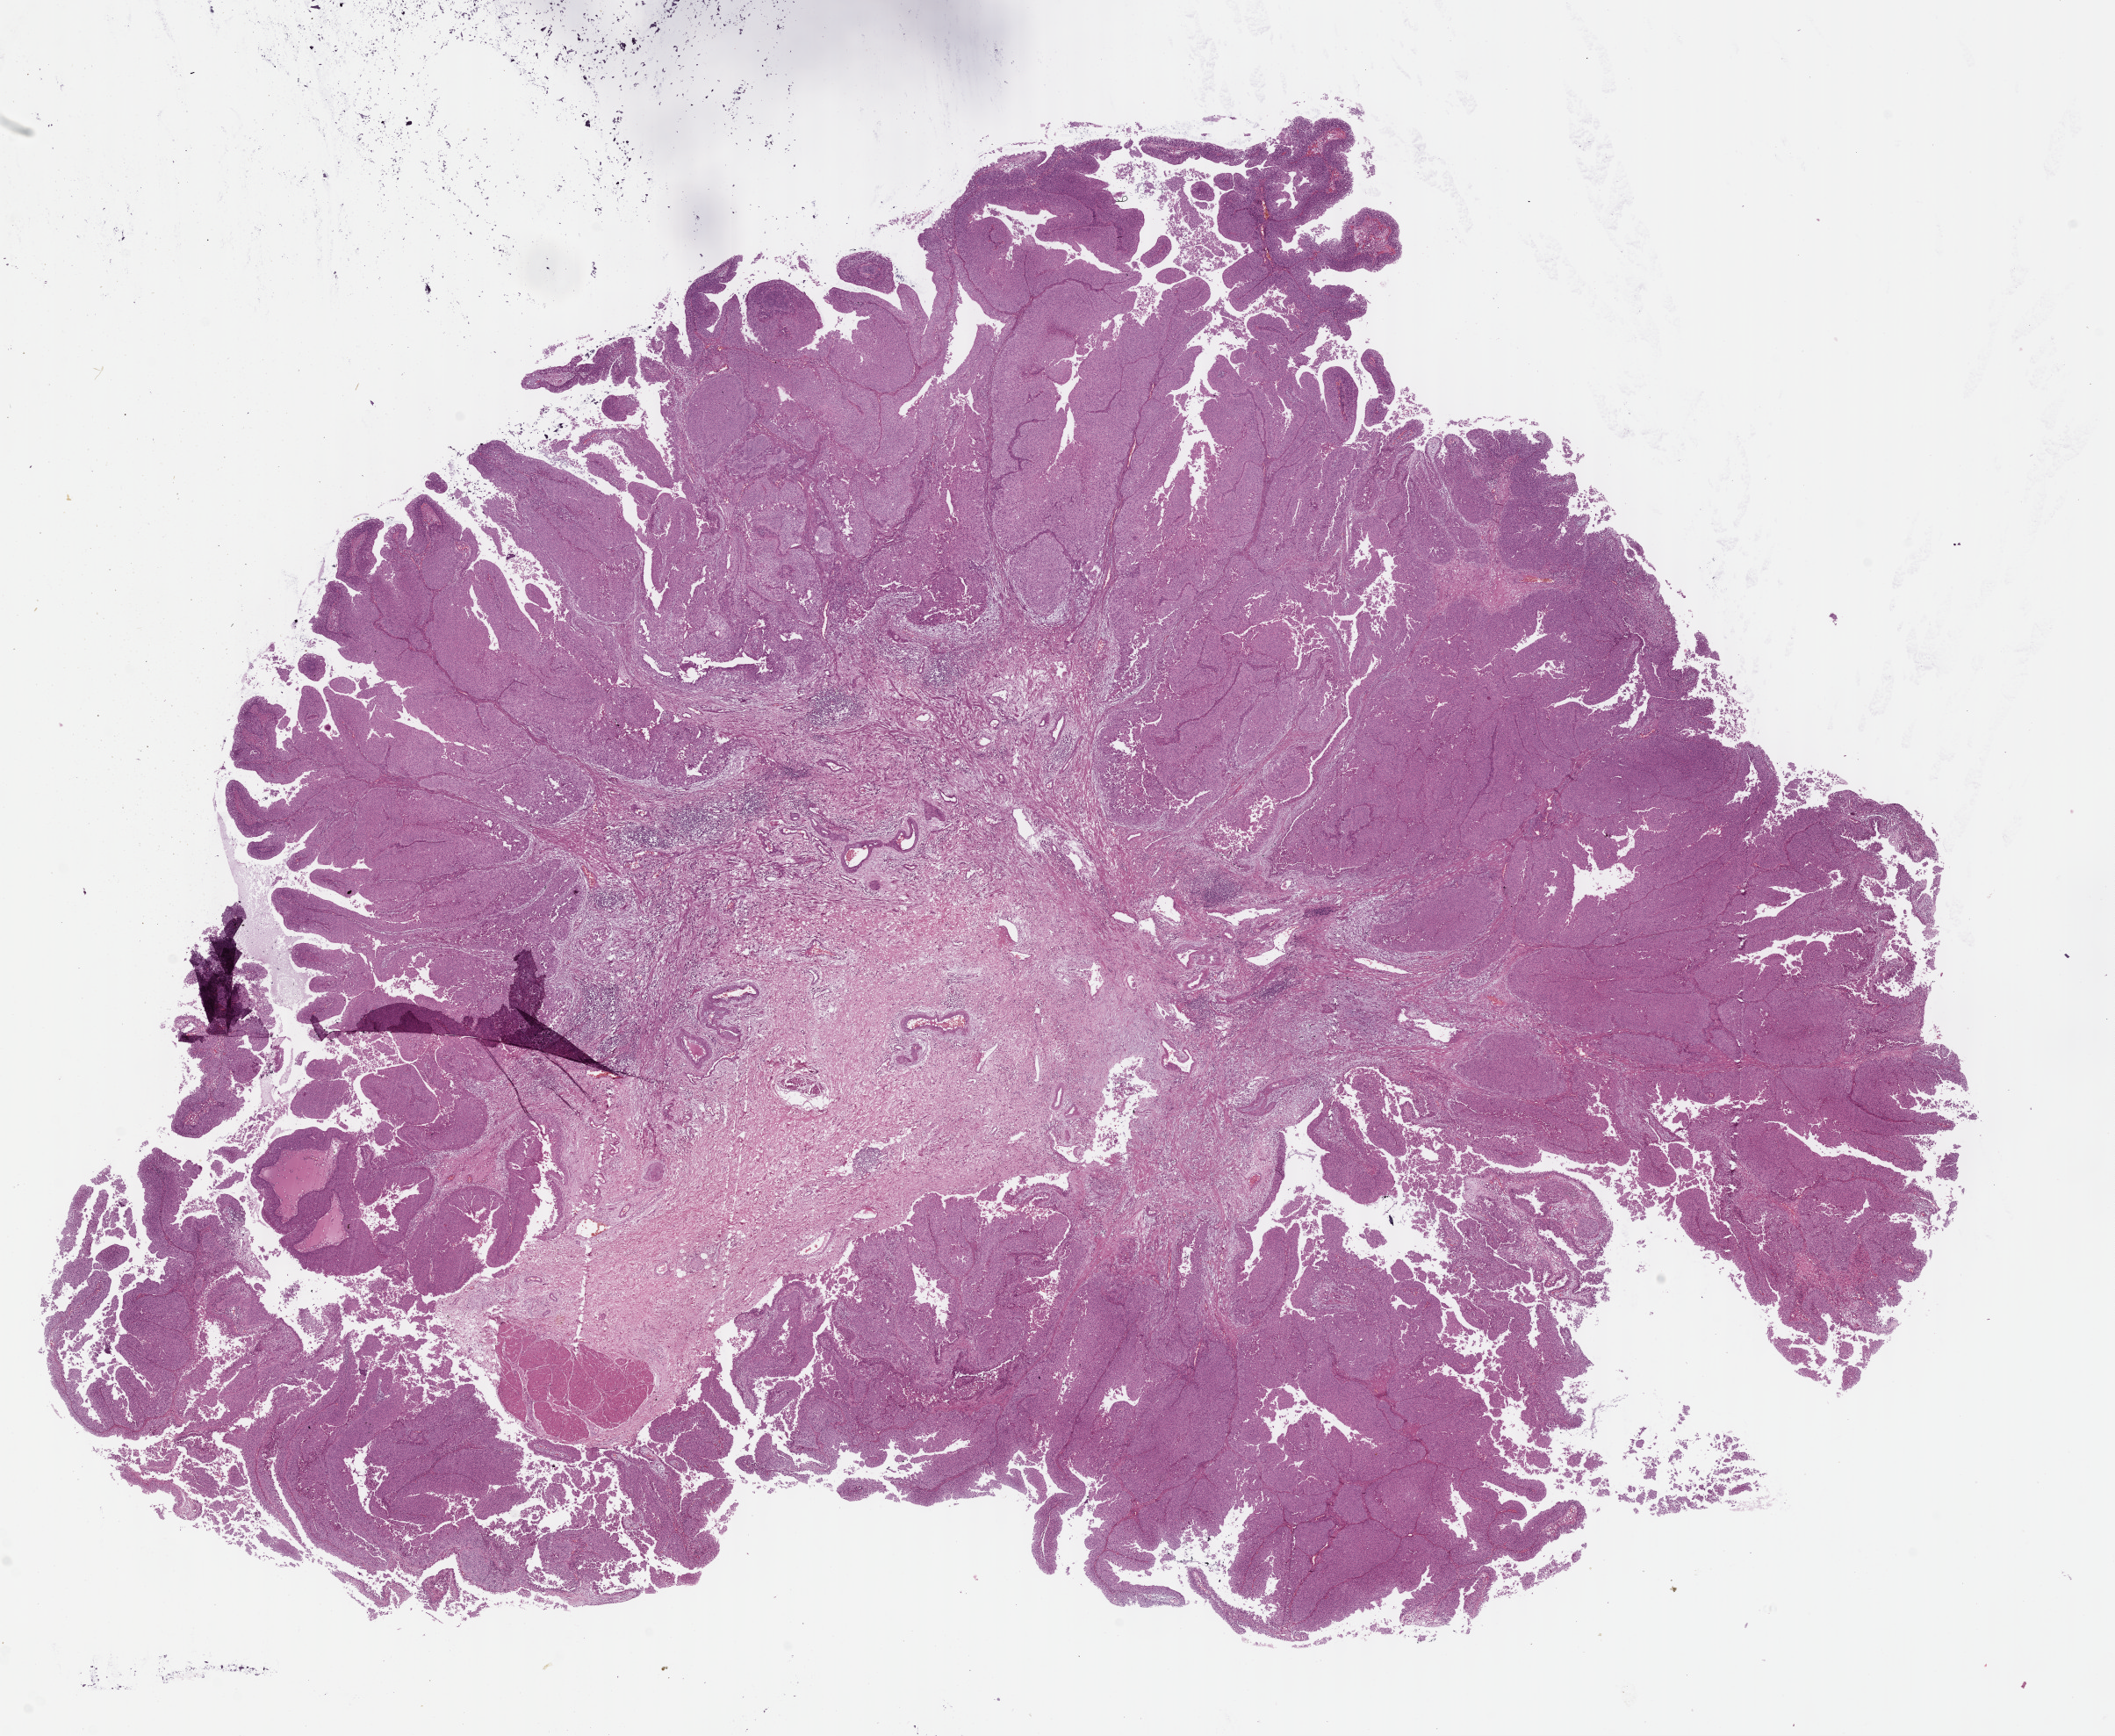
Hematoxylin and eosin (H&E) stained whole-slide image — a low-resolution overview of the entire scanned area, about 18.9 x 15.5 mm (from a 40x scan), formalin-fixed paraffin-embedded (FFPE) diagnostic section, bladder, primary tumour sample. Male patient; age at initial diagnosis 67 years. Histologic grade: low grade.
Pathologic diagnosis: Transitional cell carcinoma. AJCC pathologic stage: II.